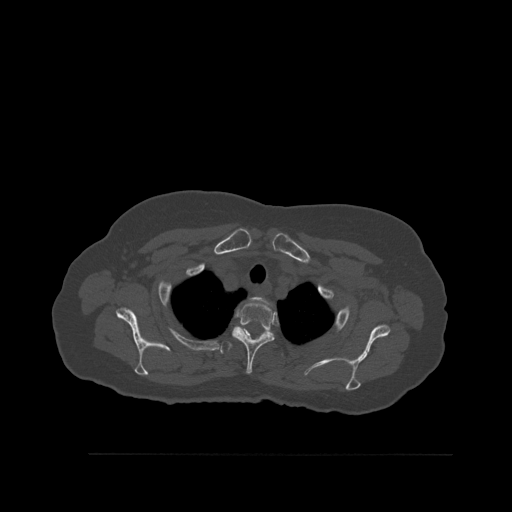
CT including the spine, one axial slice; position 430 of 527 along the scan axis; bone window (W 1800 / L 400 HU); 1.5 mm slice thickness; 512 × 512 image matrix, field of view 470 × 470 mm. Patient: female, 73 years. Case-level facts recorded for this patient, not image findings: primary cancer: breast; vertebrae with lytic lesions (as recorded): L2.
Structures marked on this image (semi-automatic segmentation, software-assisted and operator-edited):
- T1 vertebra: box from (x=252, y=297) to (x=269, y=304) px
- T2 vertebra: (x=230, y=300)–(x=275, y=374)
- T3 vertebra: (x=220, y=341)–(x=284, y=357)